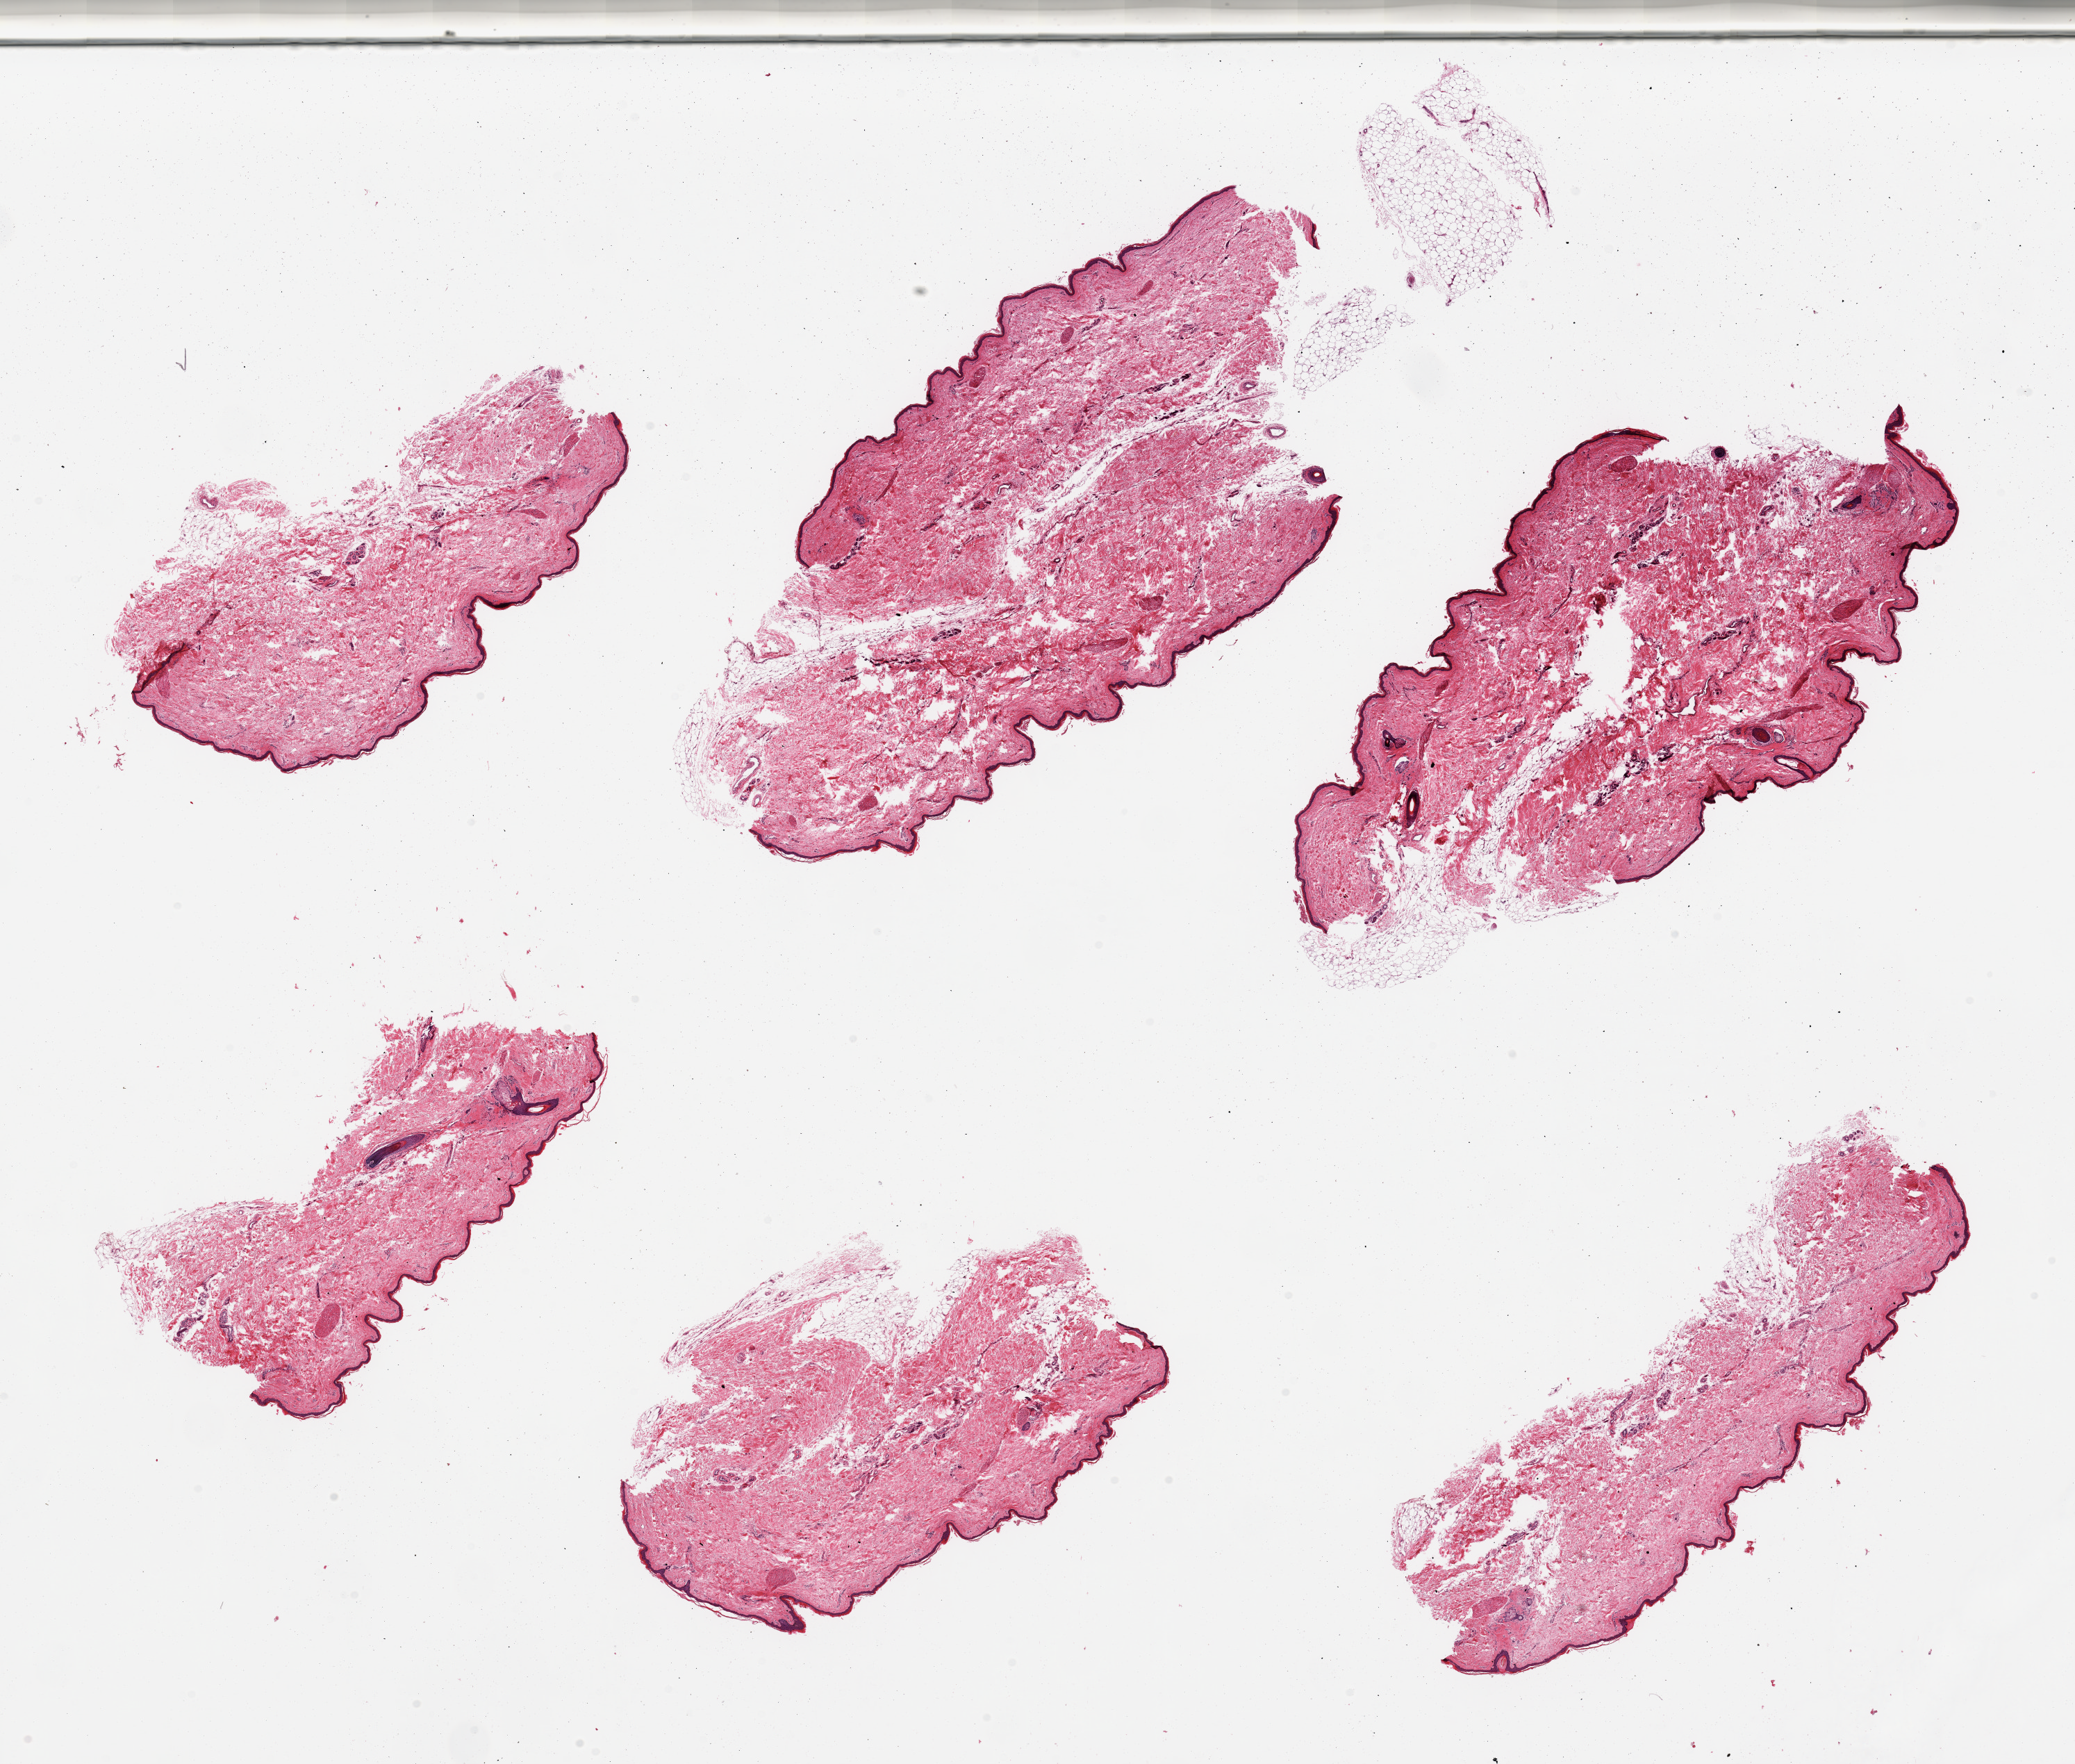
Digitized haematoxylin and eosin-stained section — whole scanned area (about 23.6 x 20.1 mm, from a 20x scan) shown as a low-resolution overview. PAXgene-fixed paraffin-embedded (PFPE) section. Section of skin of lower leg (target tissue). Tissue donor sample. Male donor.
• reviewer comment on this tissue sample: 6 pieces; 10% dermal fat; no sign of sclerosis or vasculitis